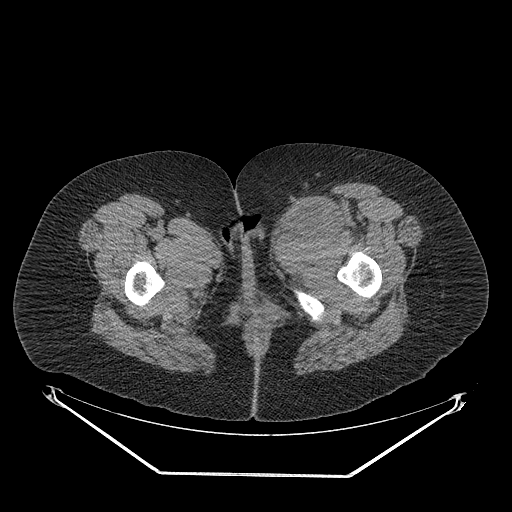
CT of an extremity soft-tissue mass (from a PET/CT study), one axial slice; position 41 of 267 along the scan axis; reconstruction kernel STANDARD; soft-tissue window (W 400 / L 40 HU); 3.75 mm slice thickness; 512 × 512 image matrix, field of view 500 × 500 mm. Female patient. Case-level facts recorded for this patient, not image findings: histological type: myxofibrosarcoma; grade: intermediate; site of the primary tumour: left thigh.
Annotated regions visible in this slice (expert contour drawn on MRI and transferred to this co-registered scan by the dataset authors):
- gross tumour volume including surrounding oedema: bounding box [x1, y1, x2, y2] px = [265, 199, 359, 254]
- gross tumour volume (mass): [278, 199, 341, 241]